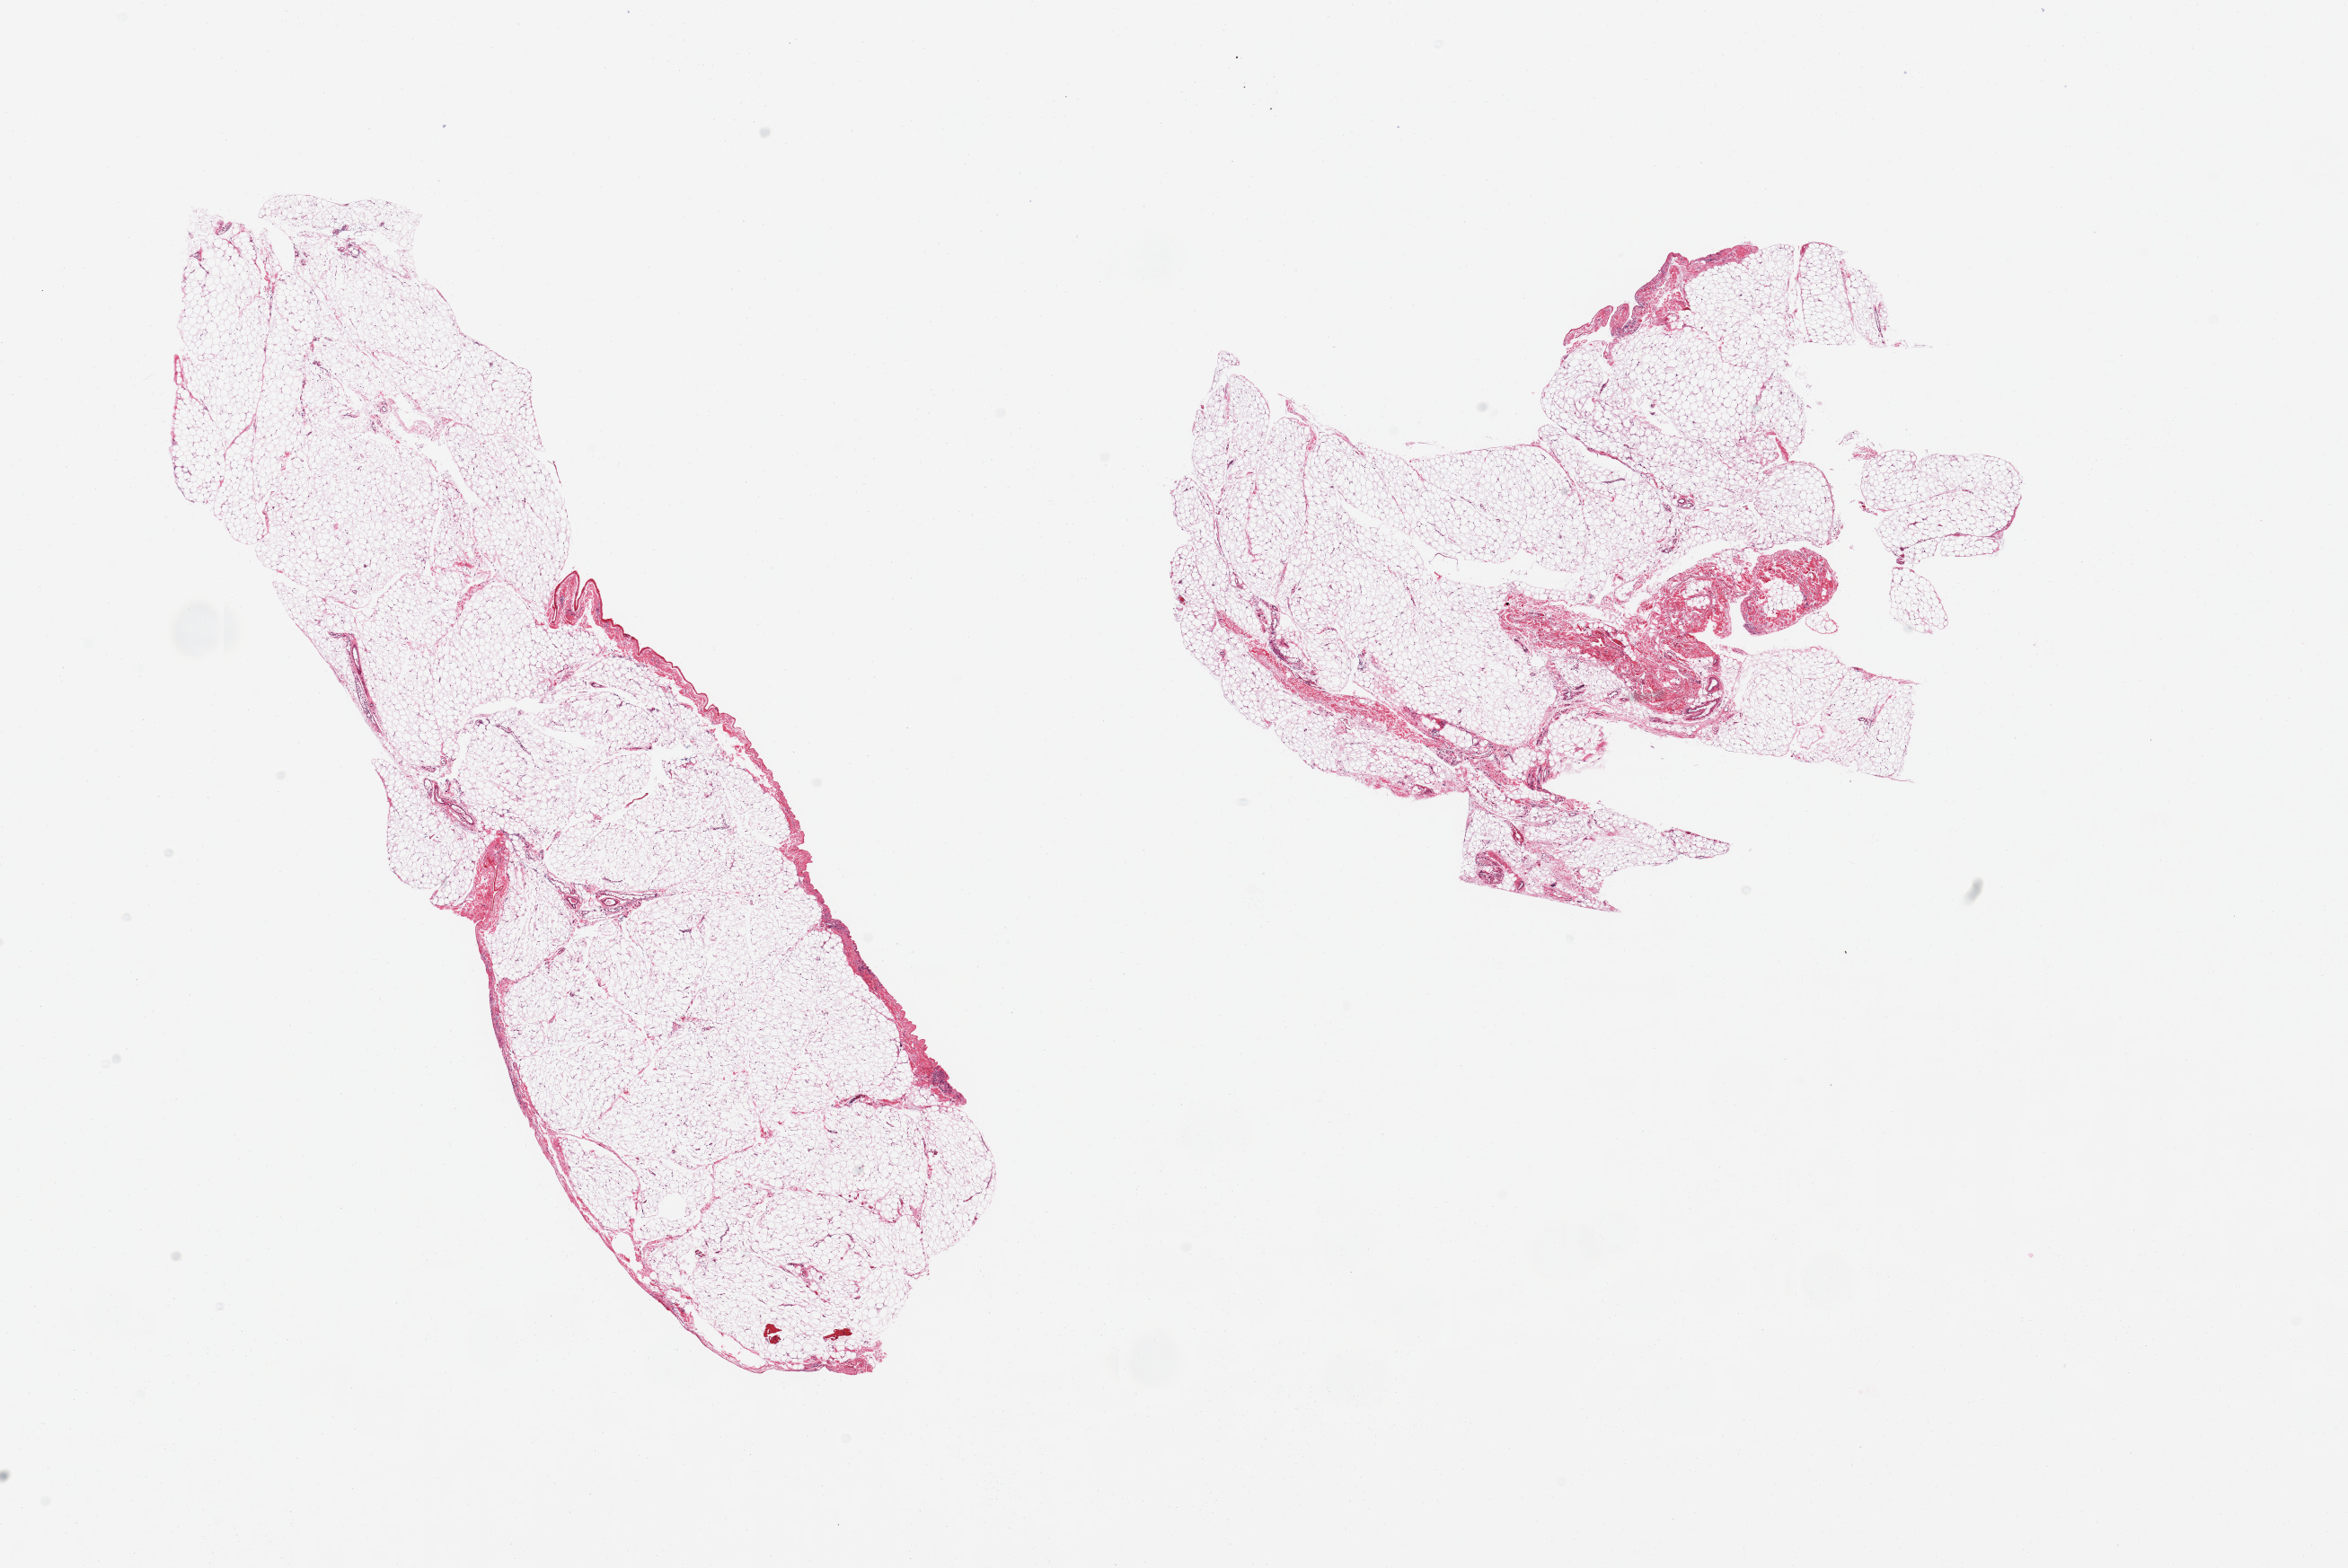
Digitized hematoxylin and eosin (H&E)-stained section, brightfield, shown as a low-resolution overview of the whole scanned area (about 20.7 x 13.8 mm, slide scanned at 20x). PAXgene-fixed, paraffin-embedded tissue. Section of omentum (target tissue). Tissue donor sample. Donor: male.
Reviewer comment on this tissue sample: 2 pieces, ~10-15% fascia/mesothelial hyperplasia.